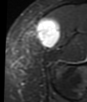
MRI of an extremity soft-tissue mass, one axial slice; slice 16 of 48 in the series (ordered by position); STIR; MR volume resampled by the dataset authors to the PET/CT grid (not the native acquisition matrix); 3.27 mm slice thickness; 87 × 102 image matrix, field of view 85 × 100 mm. Female patient. Case-level facts recorded for this patient, not image findings: histological type: synovial sarcoma; grade: intermediate; site of the primary tumour: right thigh.
Annotated regions visible in this slice (expert contour drawn on MRI and transferred to this co-registered scan by the dataset authors):
- gross tumour volume including surrounding oedema: box from (x=35, y=18) to (x=61, y=48) px
- gross tumour volume (mass): (x=35, y=18)–(x=61, y=48)